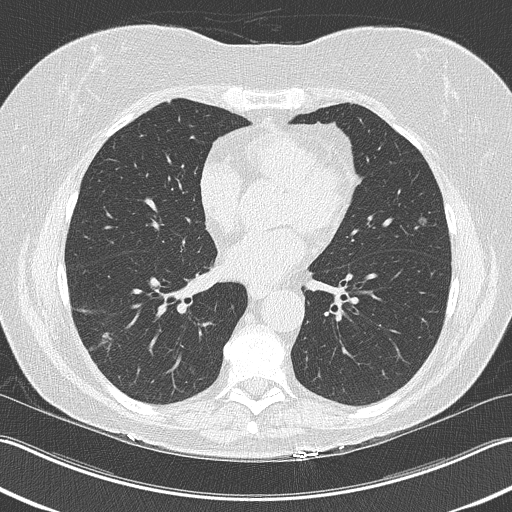
Low-dose screening chest CT, one axial slice. Position 103 of 210 along the scan axis. 120 kVp. Lung window (W 1500 / L -600 HU). 2 mm slice thickness. 512 × 512 image matrix, field of view 348 × 348 mm.
Outlined on this slice (manually delineated by an expert):
- lesion 1 (tumor, lower lobe of right lung): bounding box (x1, y1, x2, y2) in pixels: (102, 332, 112, 347)